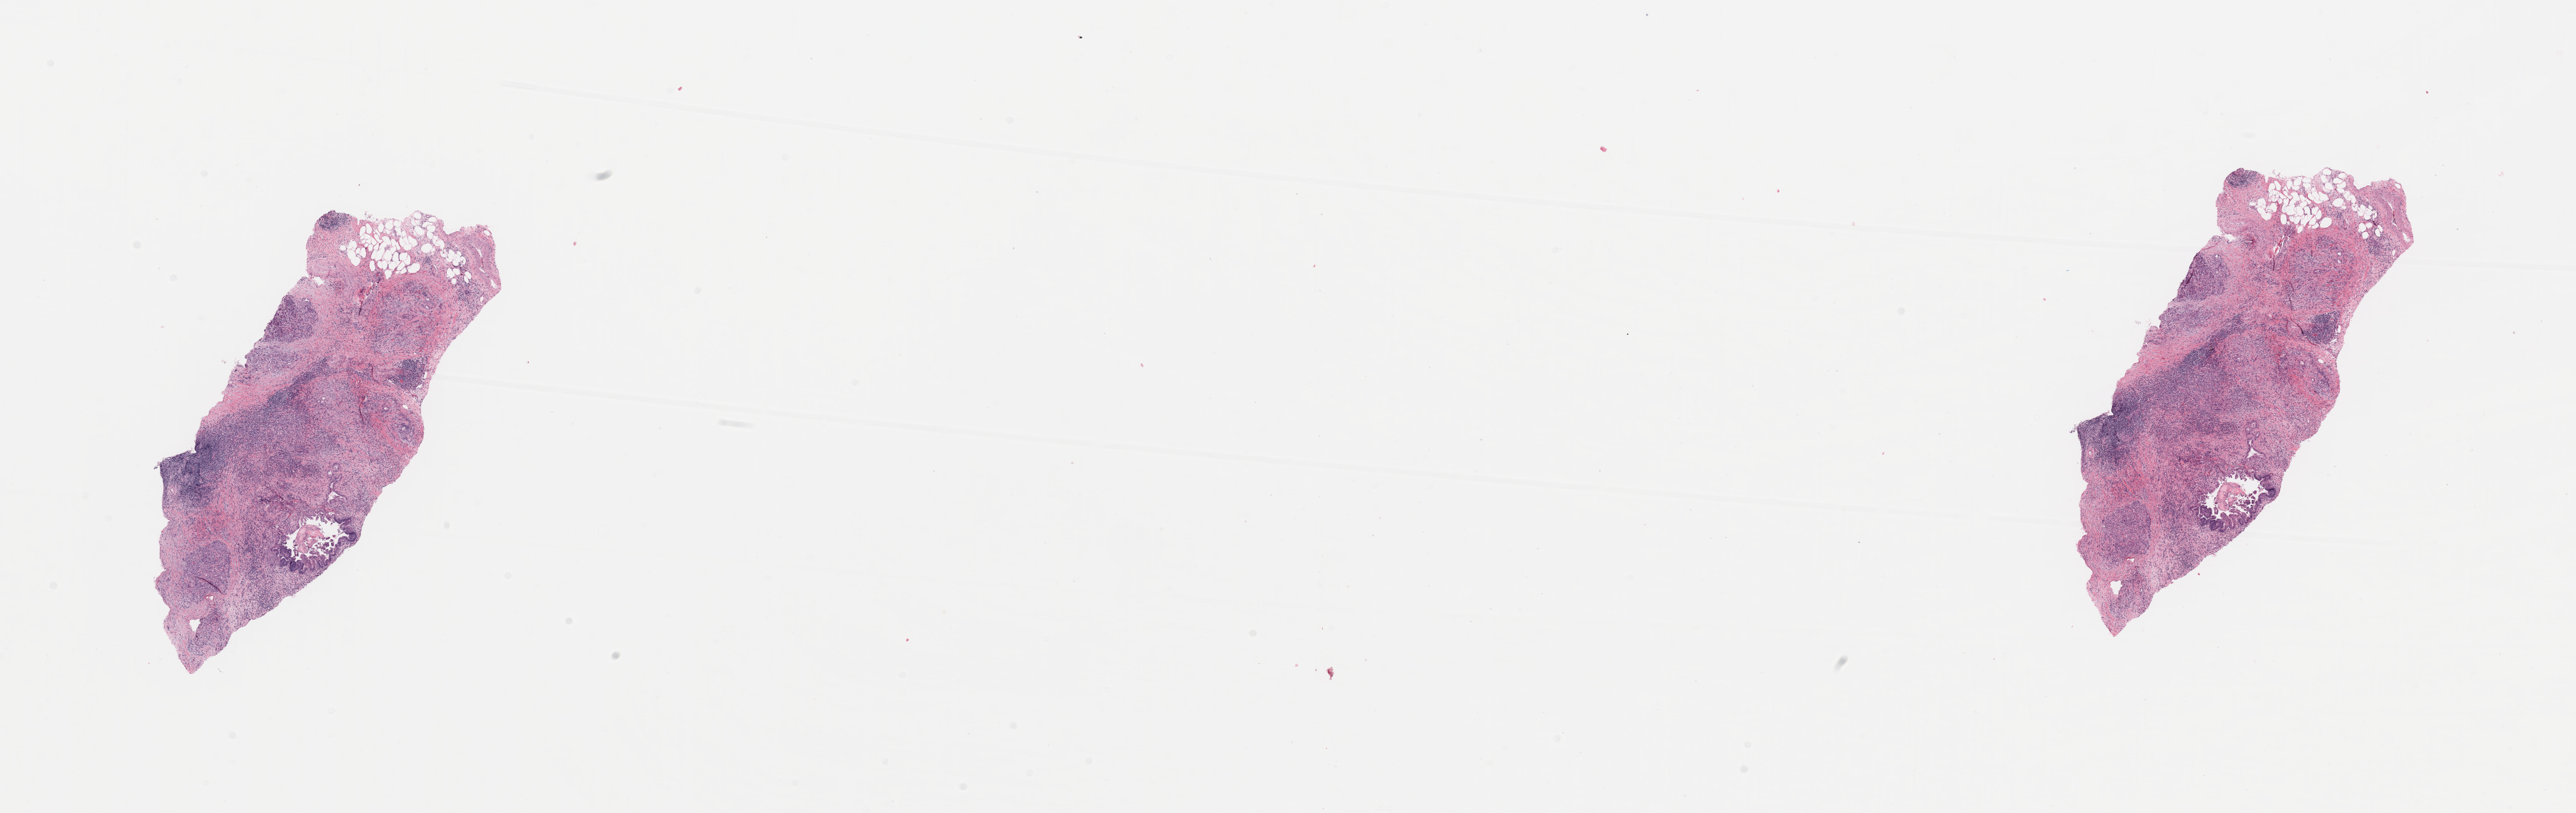
Digitized H&E-stained tissue section (whole slide) — a low-resolution overview of the entire scanned area, about 28.5 x 9.0 mm; normal (non-tumour) tissue sample, pancreas. Patient: male, age 68 years.
- this section: normal (non-tumour) tissue from the same patient
- patient diagnosis (cohort enrolment): ductal adenocarcinoma (pancreas)